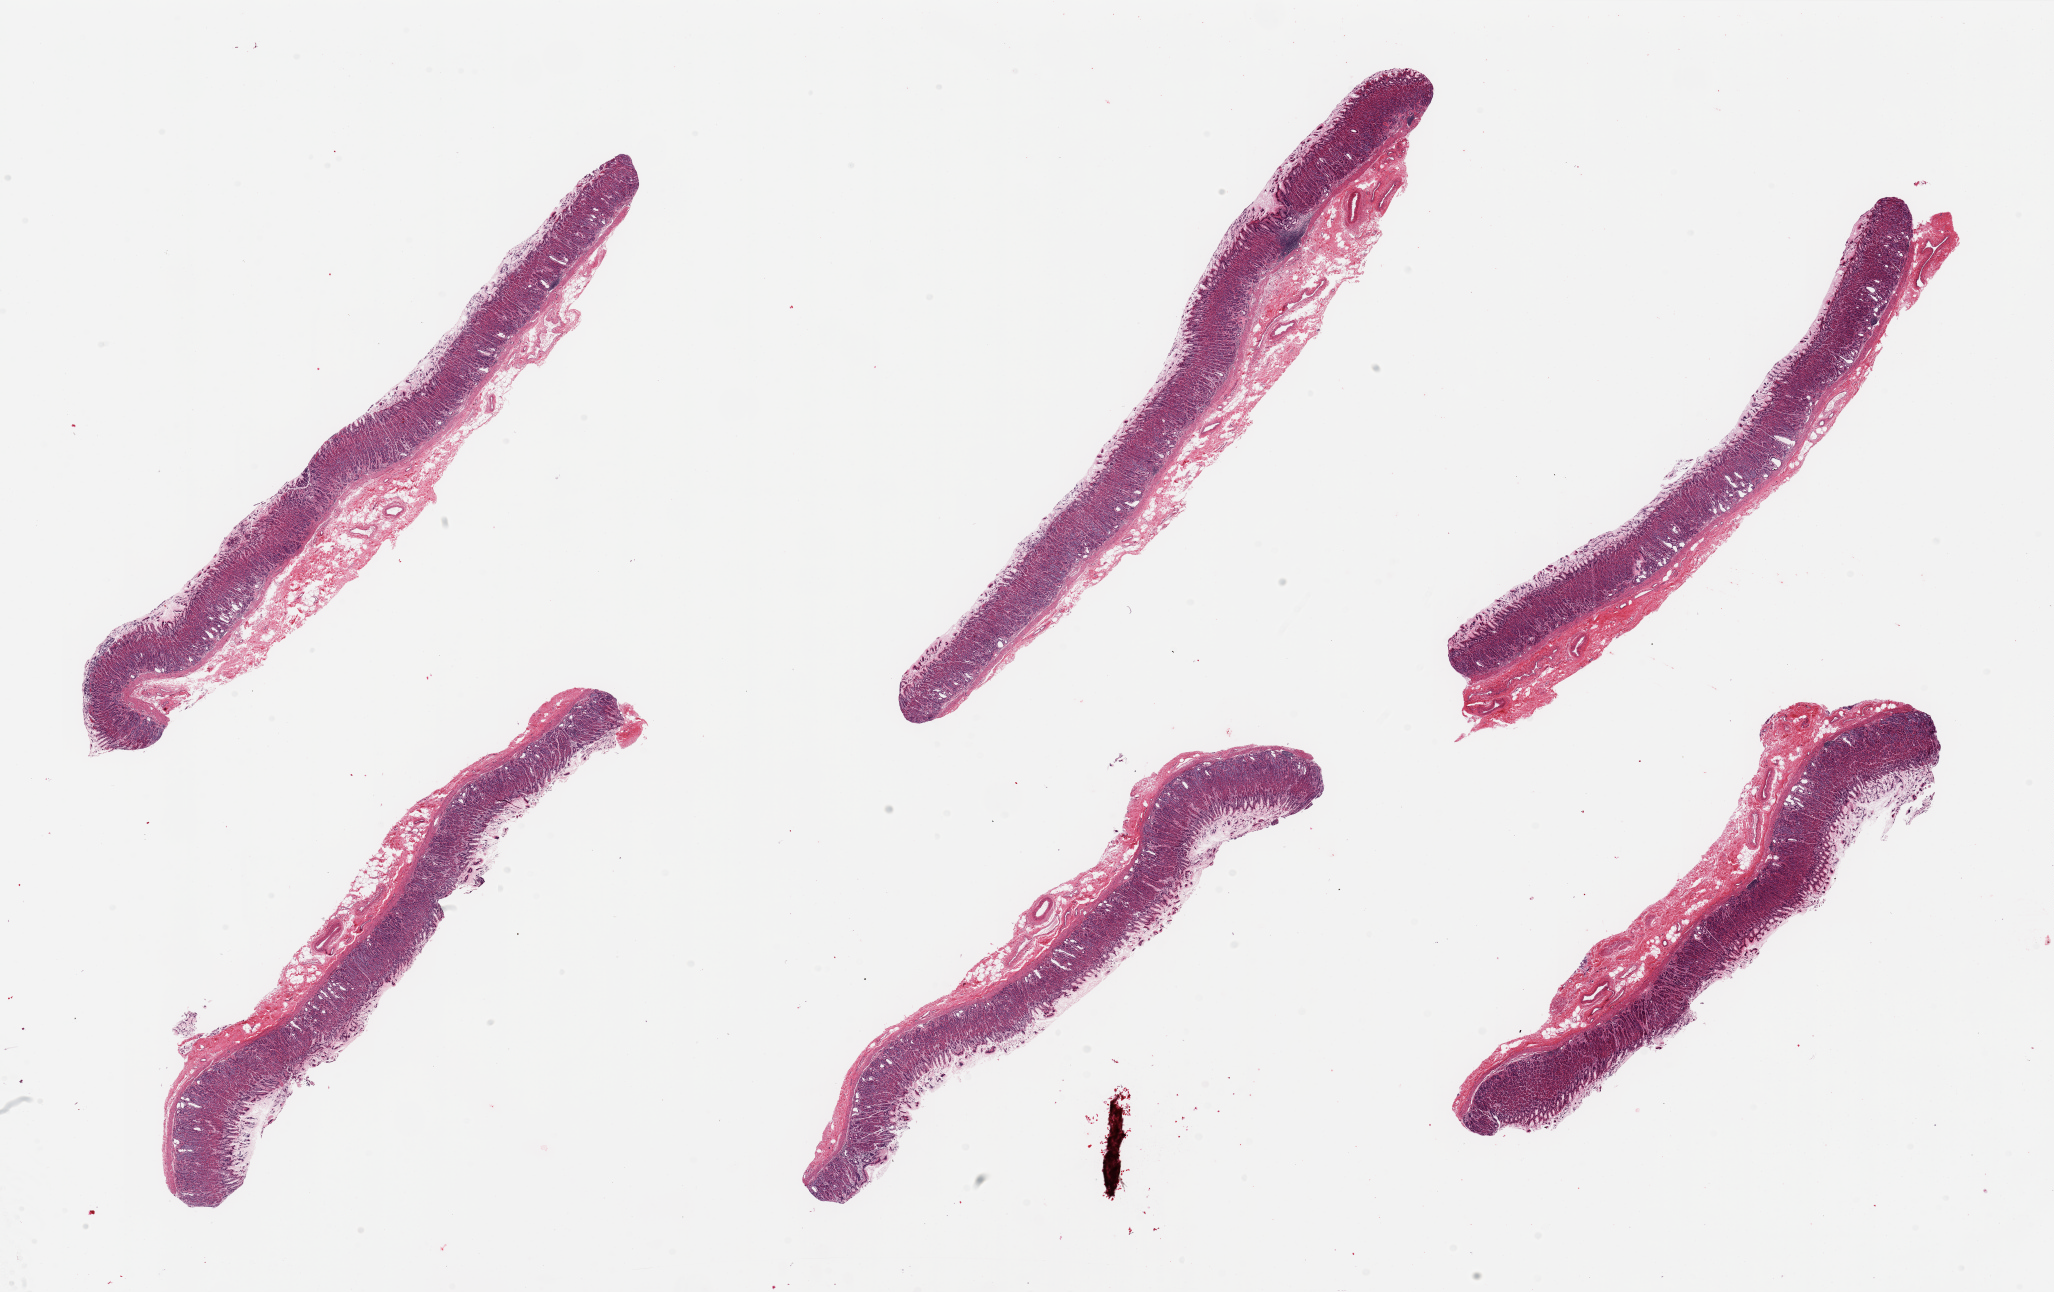
H&E whole-slide image, whole scanned area (about 32.5 x 20.4 mm) shown as a low-resolution overview, PAXgene-fixed paraffin-embedded (PFPE) section, target tissue: stomach, tissue donor sample. Donor: male.
Pathologist's review note for this sample: 6 pieces, well fixed mucosa up to ~0.8mm, ~50-80% of thickness. Incidental microcystic metaplasia in deeper glands.